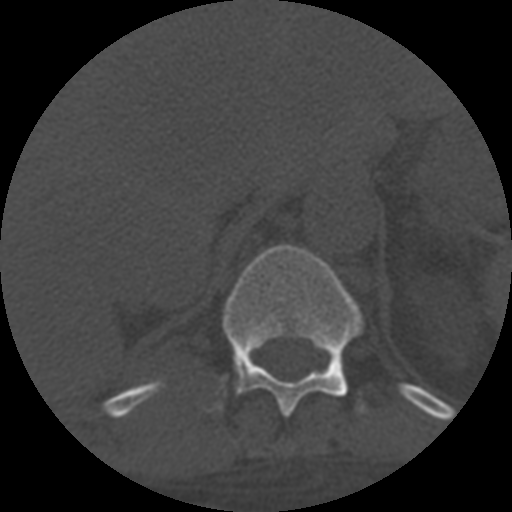
CT including the spine, one axial slice; slice 335 of 708 in the series (ordered by position); one of 3 acquisitions stored at this slice position; bone window (W 1800 / L 400 HU); 1.25 mm slice thickness; 512 × 512 image matrix. Patient age 55 years. Case-level facts recorded for this patient, not image findings: primary cancer: colon; vertebrae with lytic lesions (as recorded): T12, L1, L5.
Structures marked on this image (semi-automatic segmentation, software-assisted and operator-edited):
- T11 vertebra: bounding box <205,245,365,417> (left, top, right, bottom; pixels)